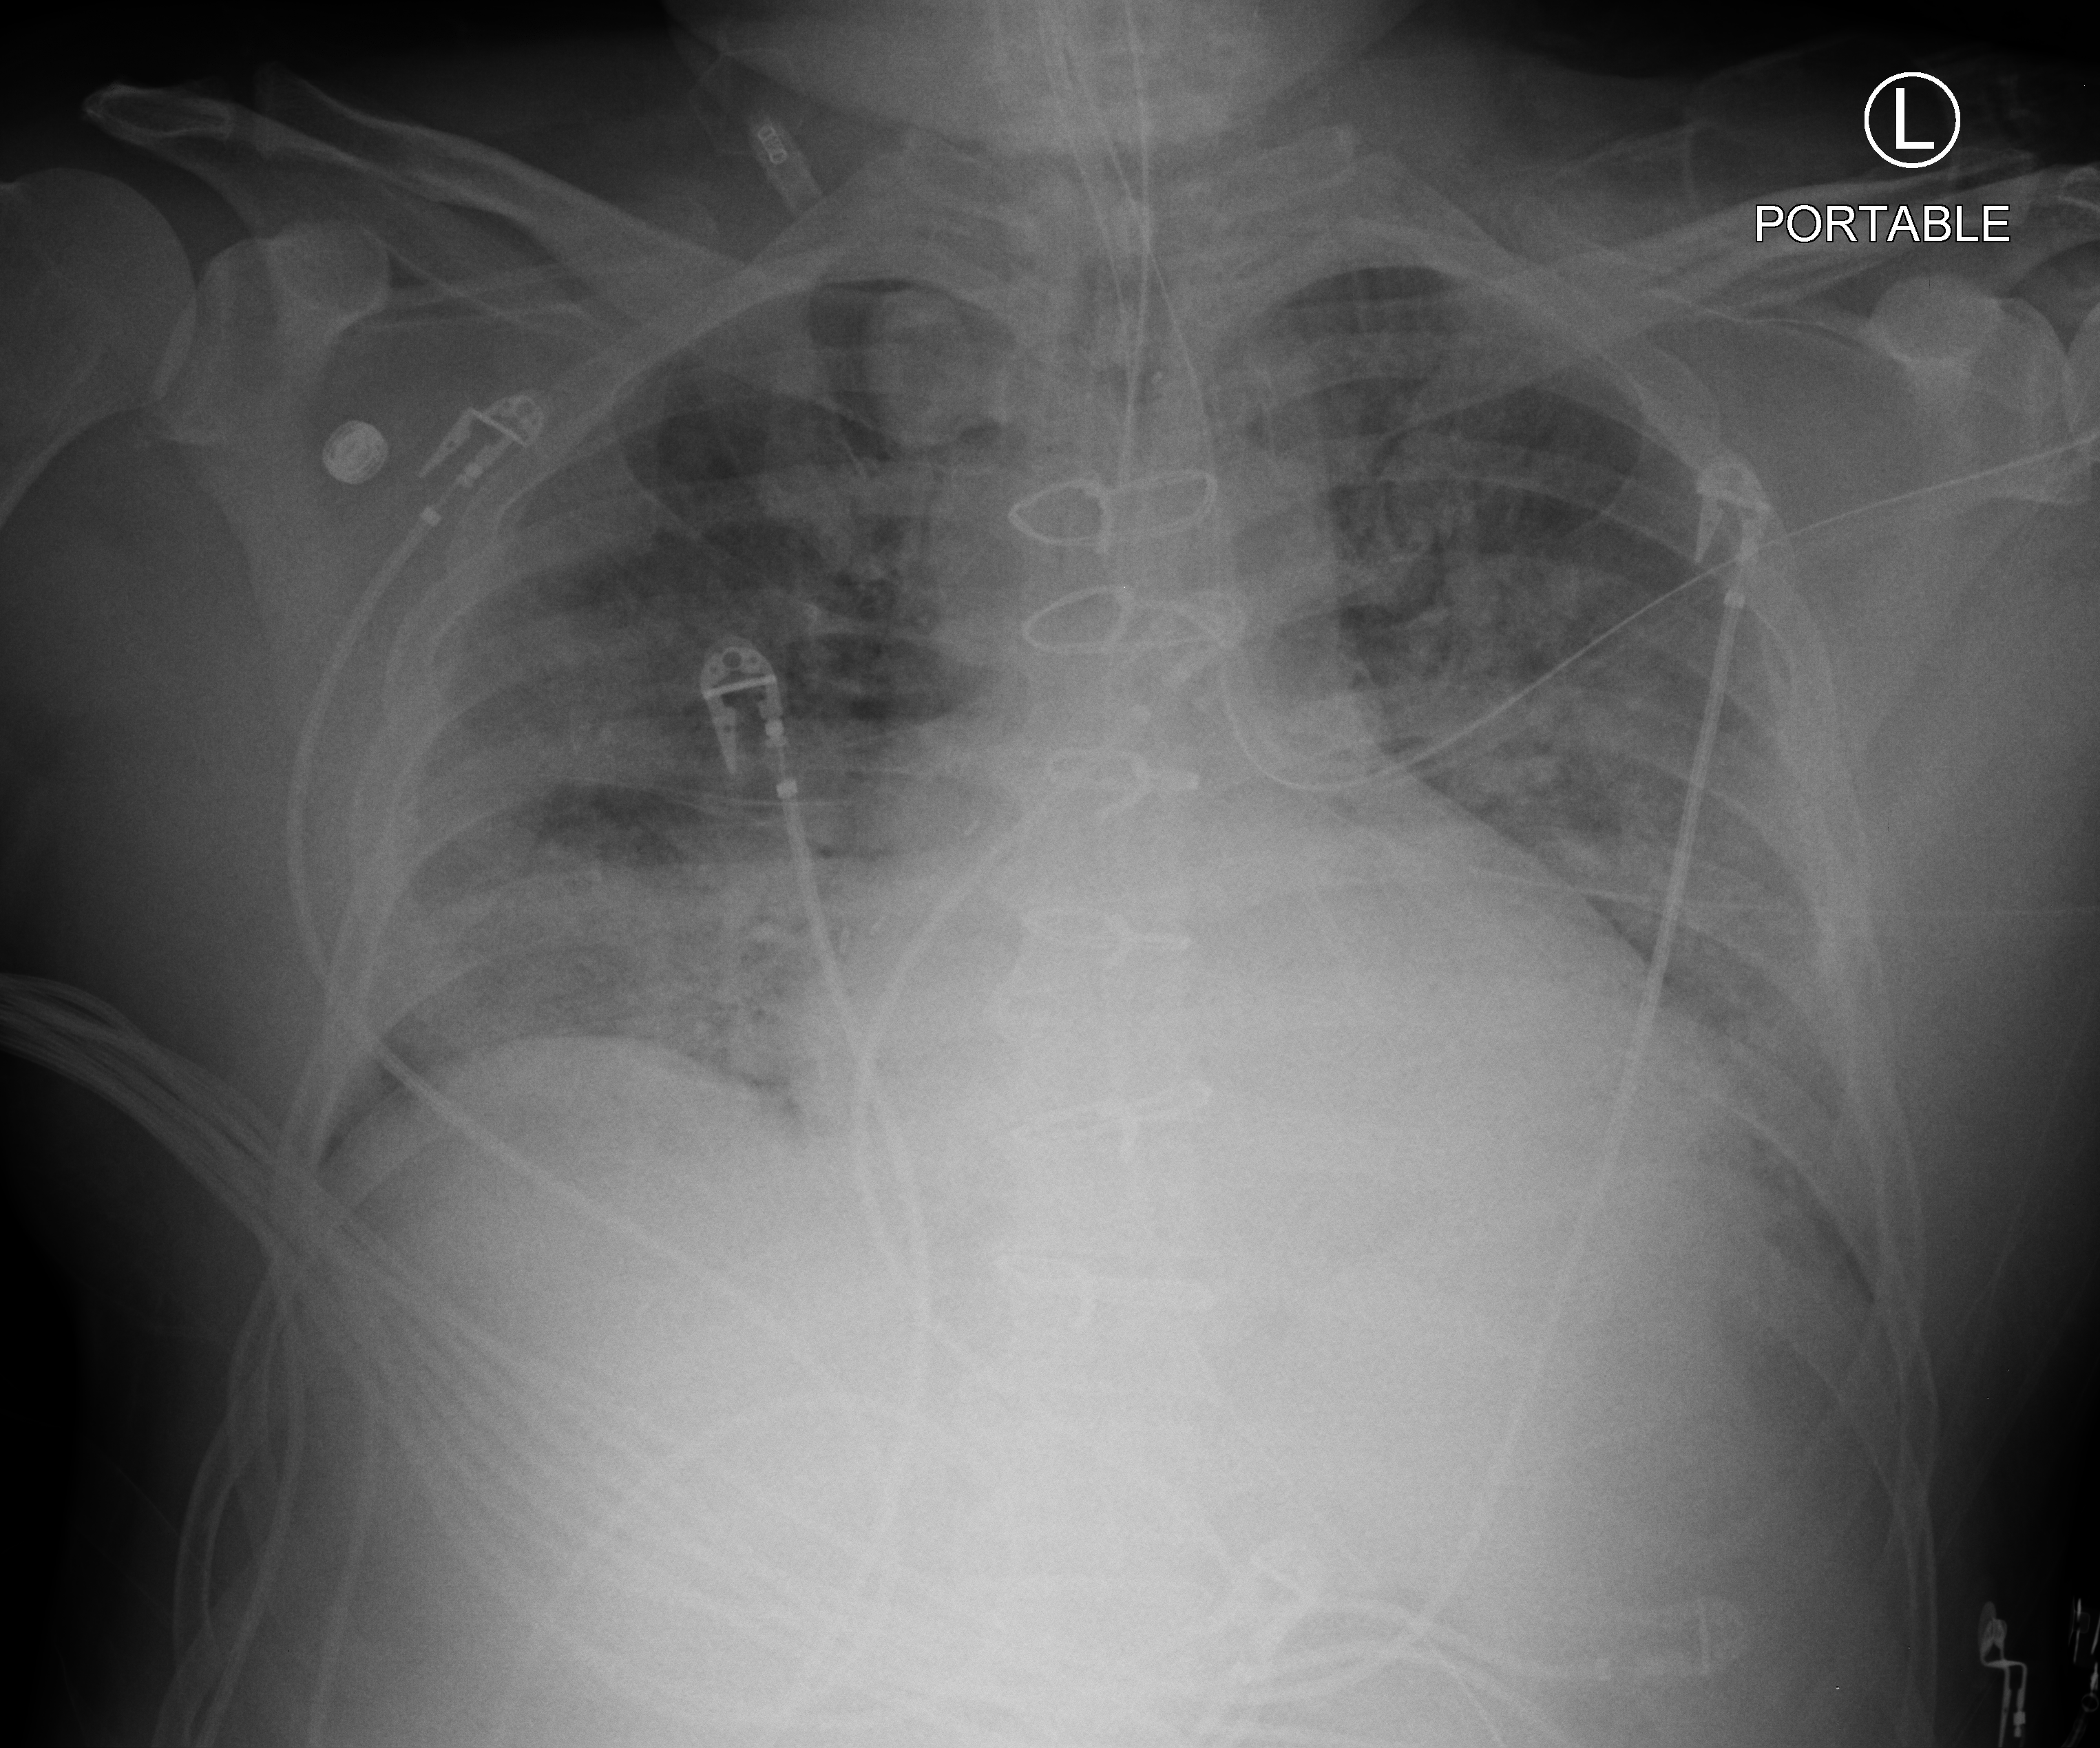
Portable chest radiograph, anteroposterior (AP) projection. Patient hospitalised with COVID-19, aged 18–59 years.
From the hospital-stay record, not from the radiograph (when in the stay this image was taken is not recorded): mechanically ventilated during this hospital stay: yes.